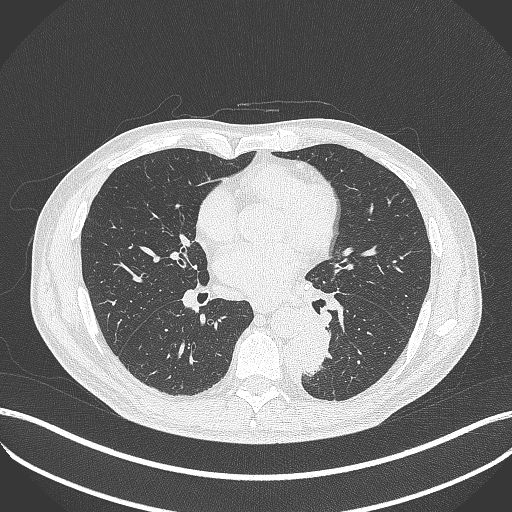
Chest CT, one axial slice. Slice 197 of 451 in the series (ordered by position). Reconstruction kernel B70f. Lung window (W 1500 / L -600 HU). 512 × 512 image matrix. Male patient, age 72 years. Case-level facts recorded for this patient, not image findings: clinical TNM (as recorded): T2b N0 M1.
Outlined on this slice (rectangle marked by the reading radiologist):
- lung tumour (recorded histology: adenocarcinoma): box from (x=298, y=322) to (x=333, y=380) px